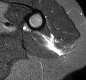
MRI of an extremity soft-tissue mass, one axial slice. Position 4 of 30 along the scan axis. STIR. MR volume resampled by the dataset authors to the PET/CT grid (not the native acquisition matrix). 3.27 mm slice thickness. 86 × 80 image matrix, field of view 84 × 78 mm. Female patient. Case-level facts recorded for this patient, not image findings: histological type: malignant fibrous histiocytoma; grade: low; site of the primary tumour: left arm.
Outlined on this slice (expert contour drawn on MRI and transferred to this co-registered scan by the dataset authors):
- gross tumour volume (mass): bounding box [x1, y1, x2, y2] px = [45, 37, 52, 46]